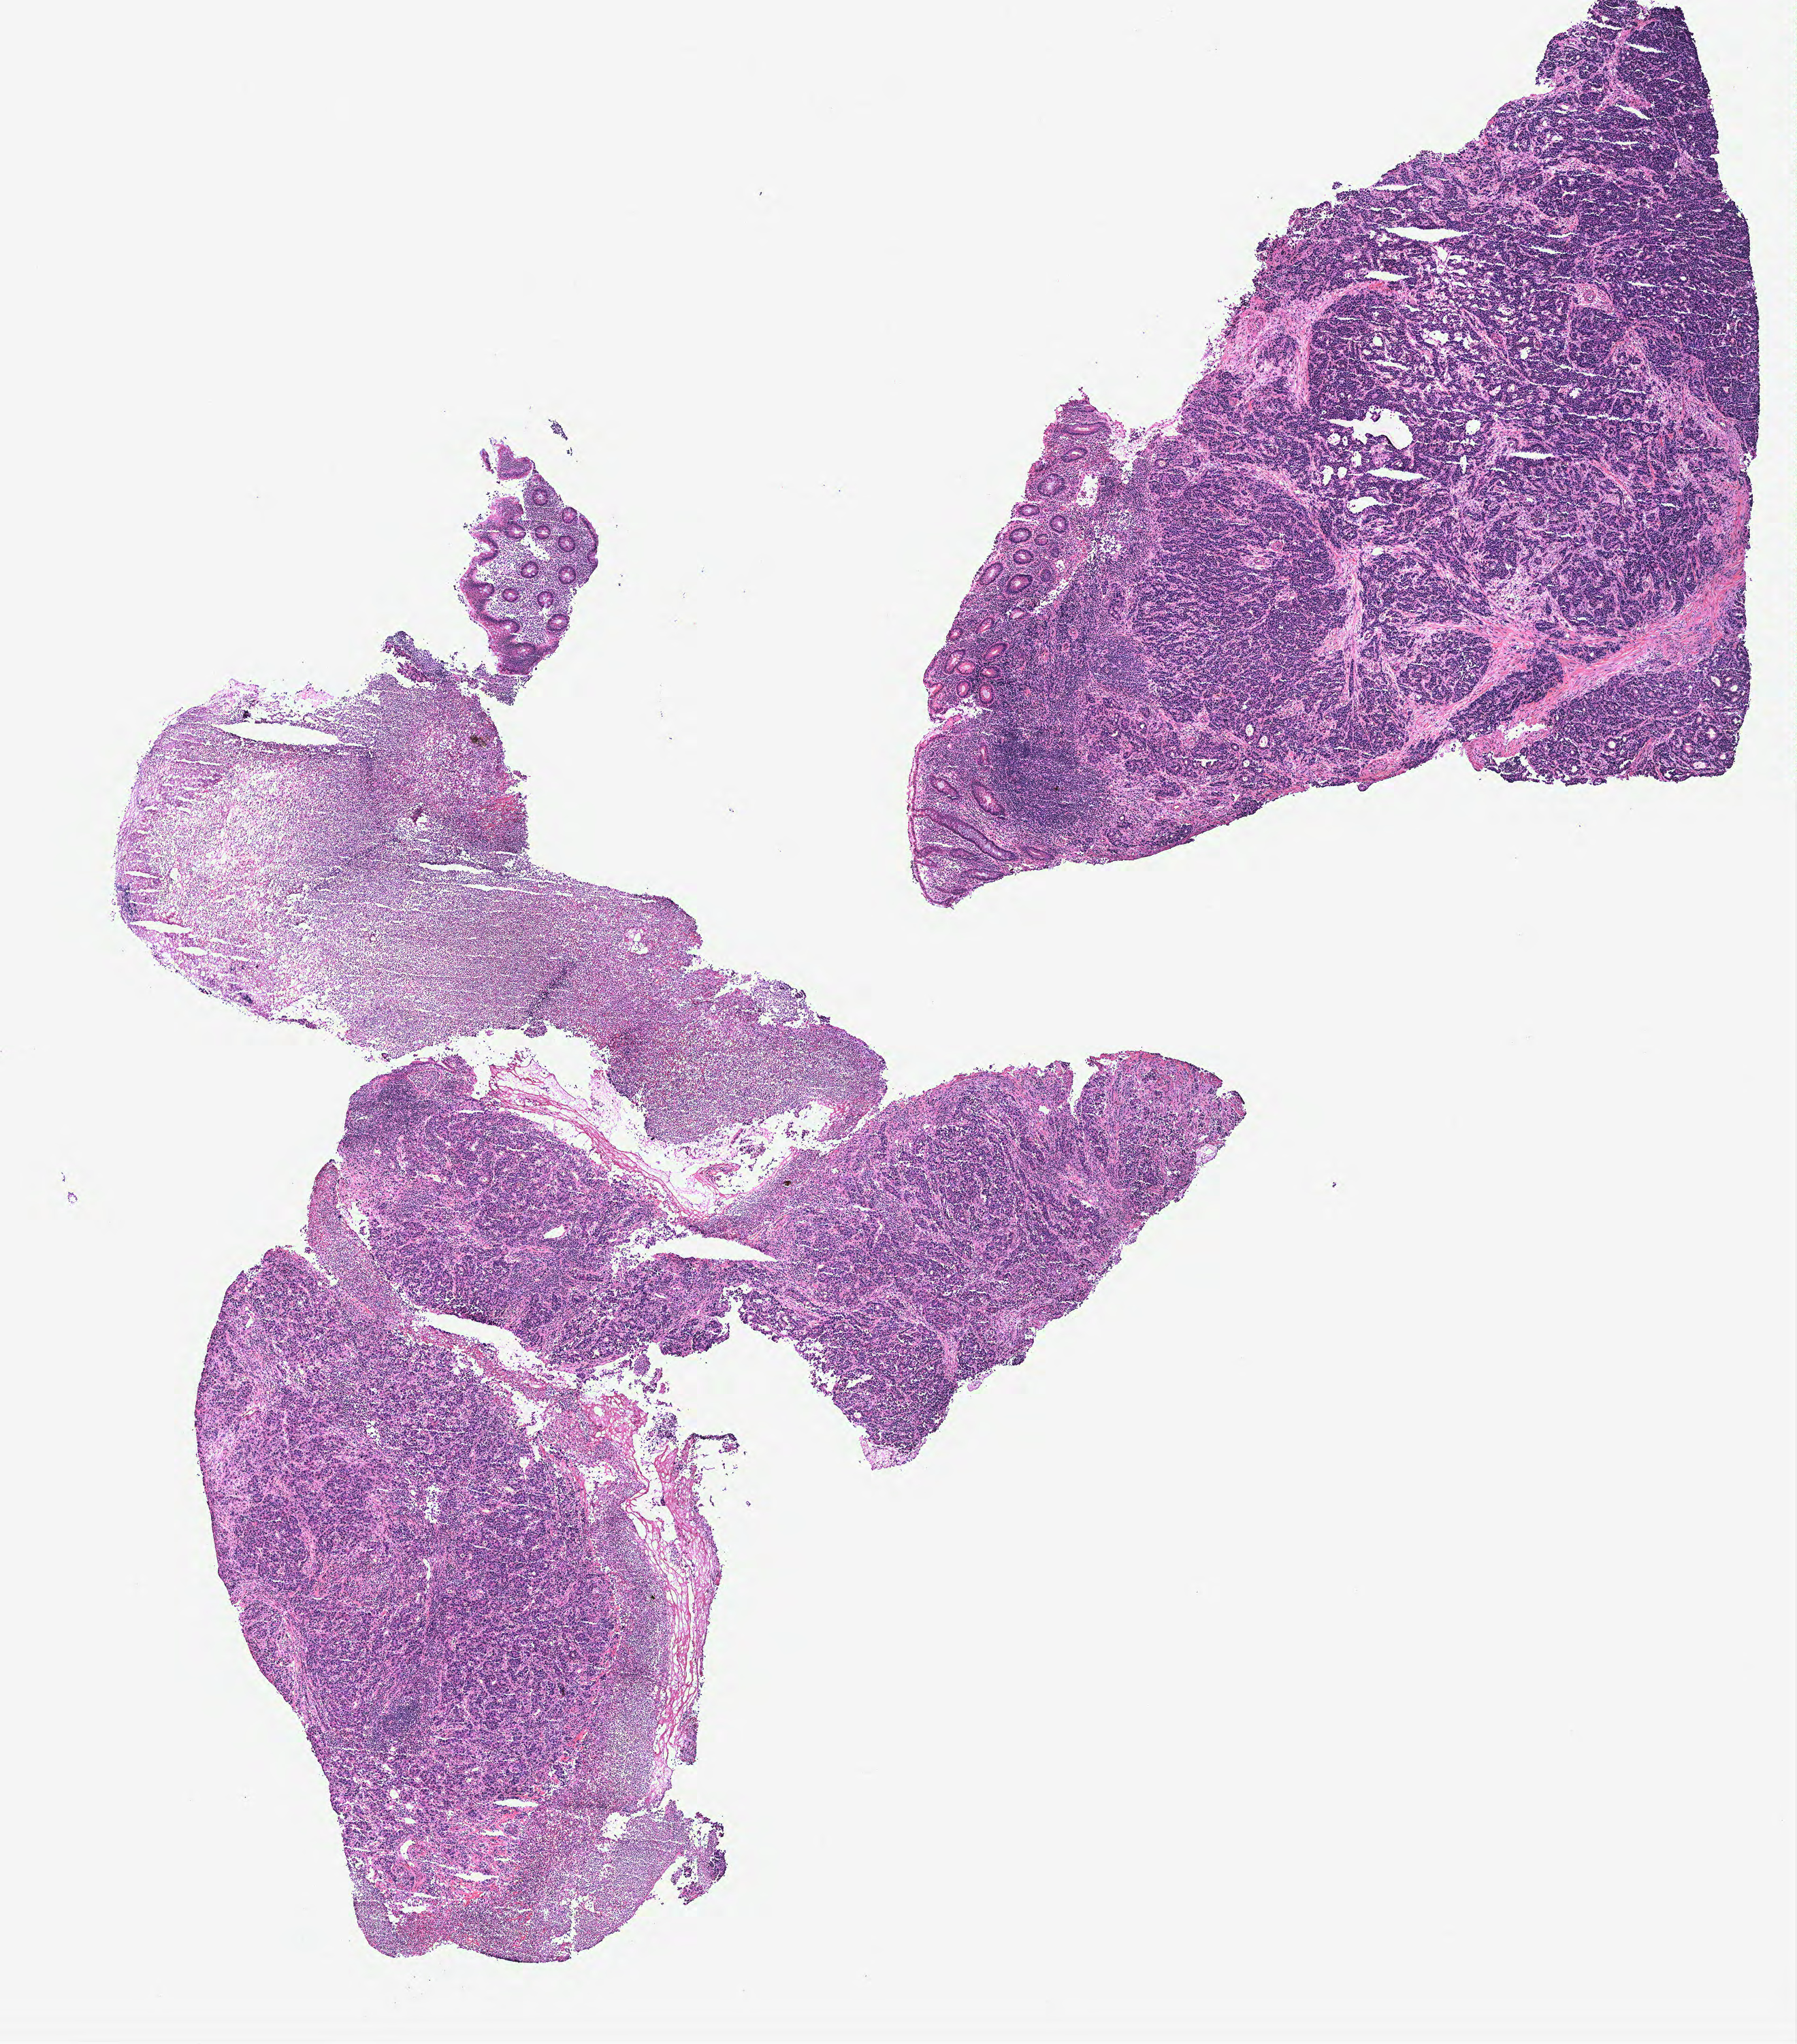
Digitized Hematoxylin and eosin (H&E) stained tissue section (whole slide), shown as a low-resolution overview of the whole scanned area (about 10.6 x 12.0 mm, acquisition: 40x scan). Colon, tissue type not recorded.
• patient diagnosis (cohort enrolment): colon cancer (colon)